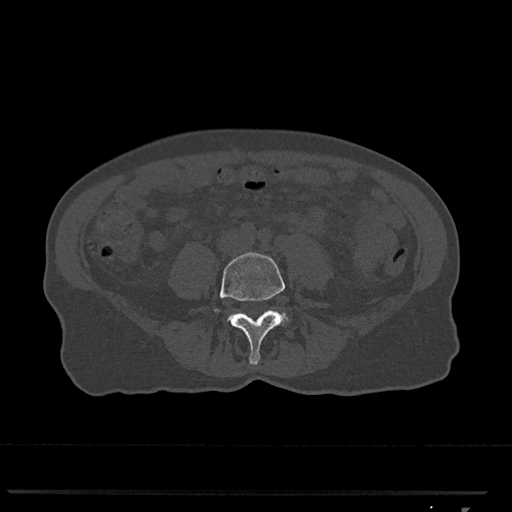
CT including the spine, one axial slice; slice 201 of 793 in the series (ordered by position); reconstruction kernel Br40s/3; bone window (W 1800 / L 400 HU); 512 × 512 image matrix. Patient: female, 62 years. From the clinical record (not read from this slice): primary cancer: renal.
Outlined on this slice (semi-automatic segmentation, software-assisted and operator-edited):
- L4 vertebra: bounding box (x1, y1, x2, y2) in pixels: (214, 252, 285, 365)
- L5 vertebra: (281, 313, 288, 321)